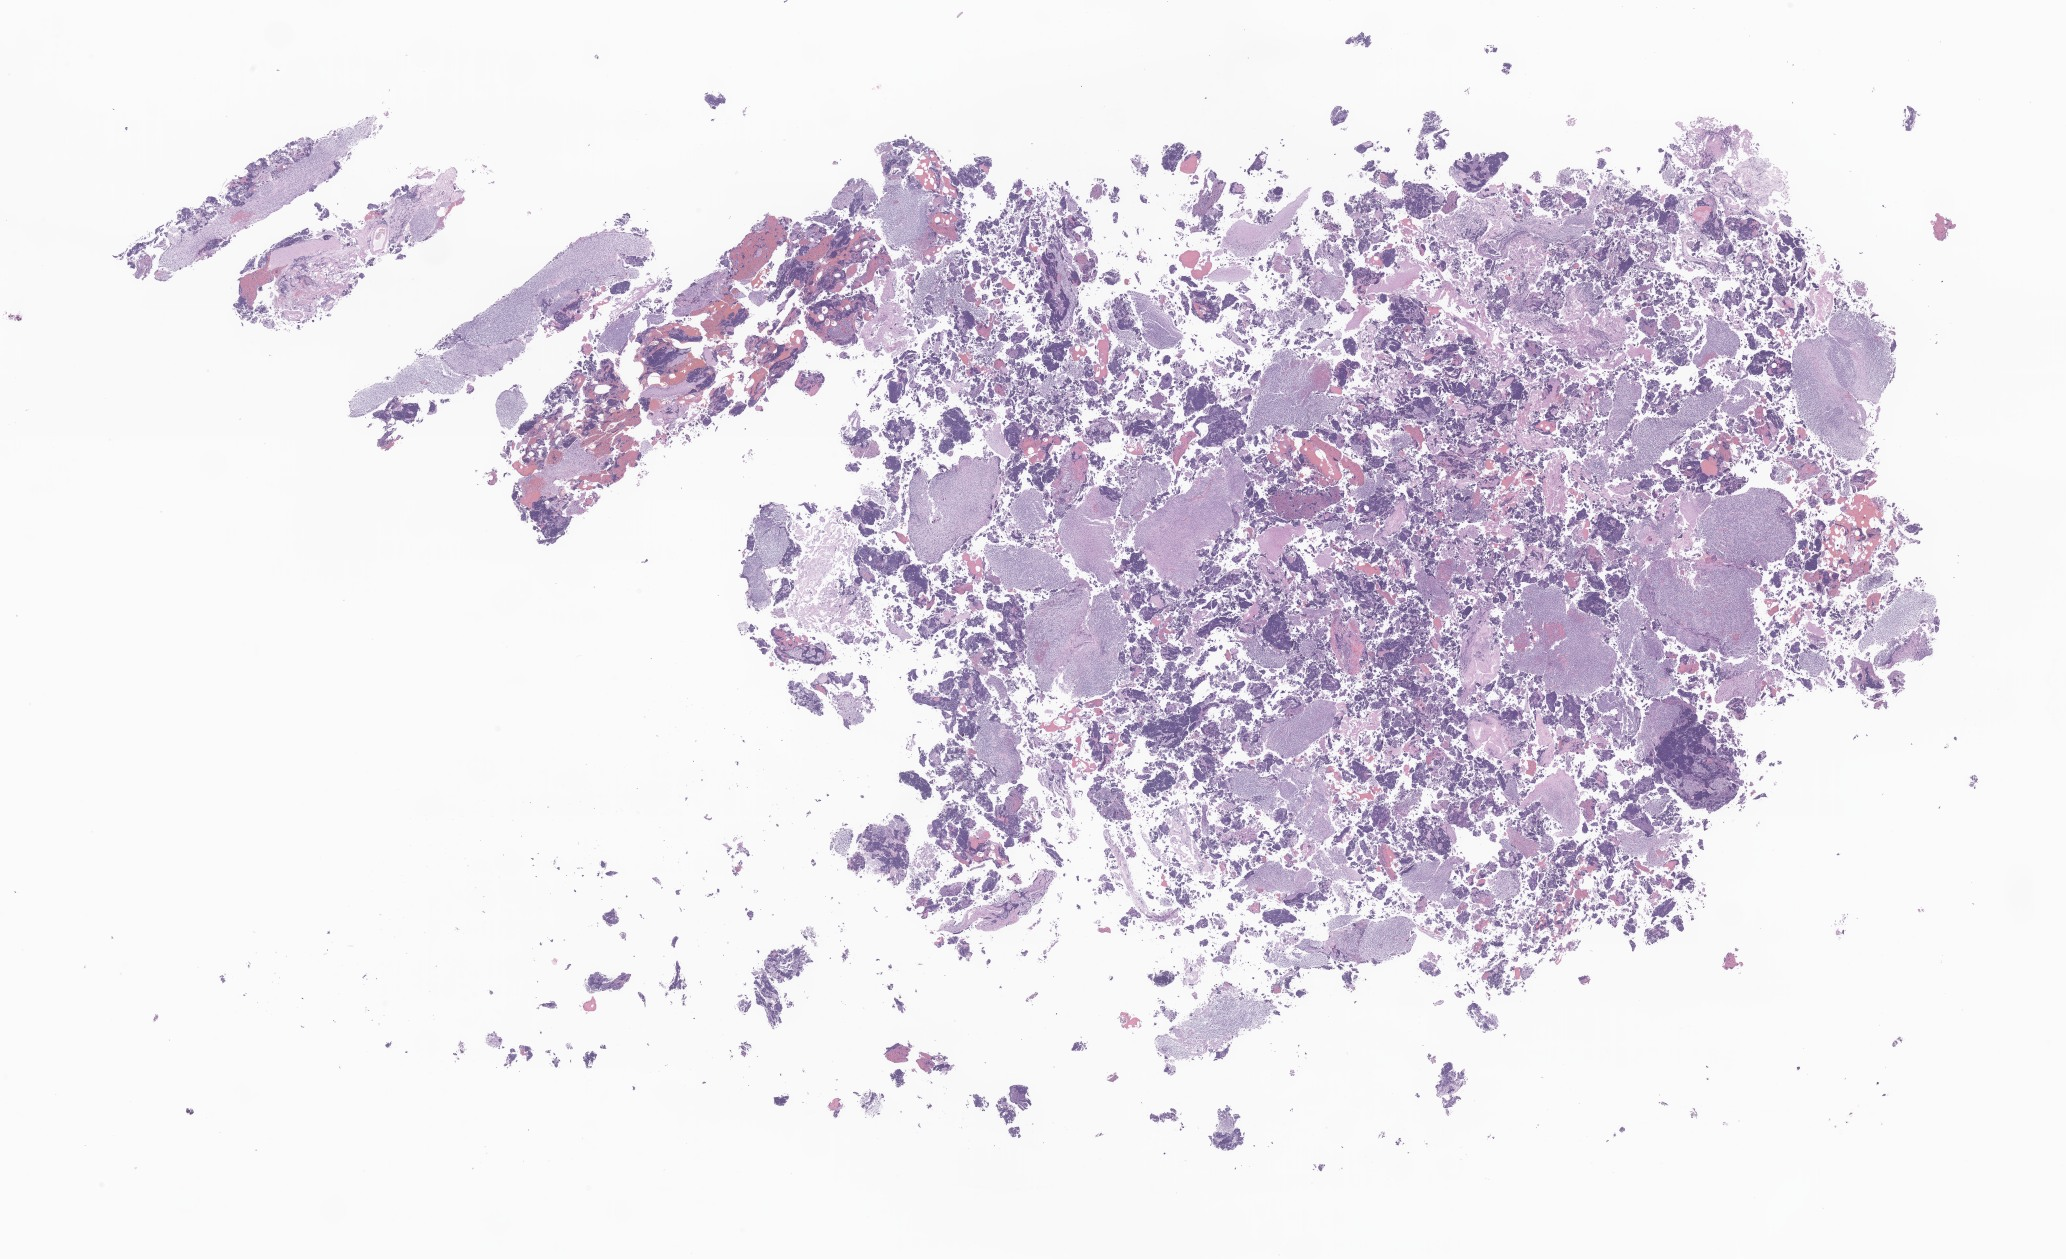
H&E whole-slide image of tumor tissue from the brain — low-resolution overview of the scanned area, about 34.9 x 21.2 mm. Formalin-fixed, paraffin-embedded (FFPE) tissue. Male patient, age 109 months (9 years 1 month).
Diagnosis (ICD-O-3 morphology term): Medulloblastoma, NOS.